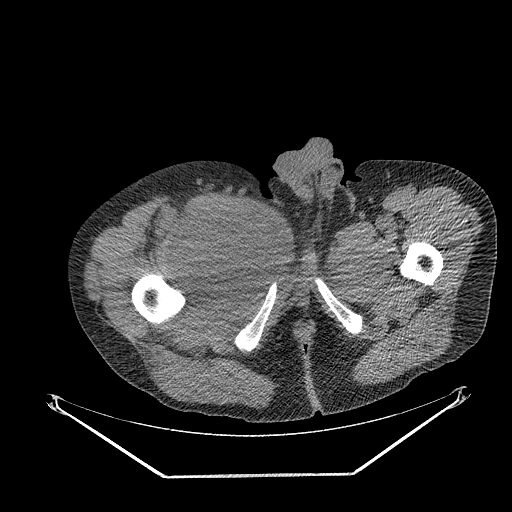
CT of an extremity soft-tissue mass (from a PET/CT study), one axial slice. Position 284 of 311 along the scan axis. Reconstruction kernel STANDARD. Soft-tissue window (W 400 / L 40 HU). 3.75 mm slice thickness. 512 × 512 image matrix. Male patient. Case-level facts recorded for this patient, not image findings: histological type: undifferentiated - pleiomorphic; grade: high; site of the primary tumour: right thigh.
Outlined on this slice (expert contour drawn on MRI and transferred to this co-registered scan by the dataset authors):
- gross tumour volume including surrounding oedema: box from (x=187, y=199) to (x=259, y=273) px
- gross tumour volume (mass): (x=187, y=203)–(x=255, y=270)